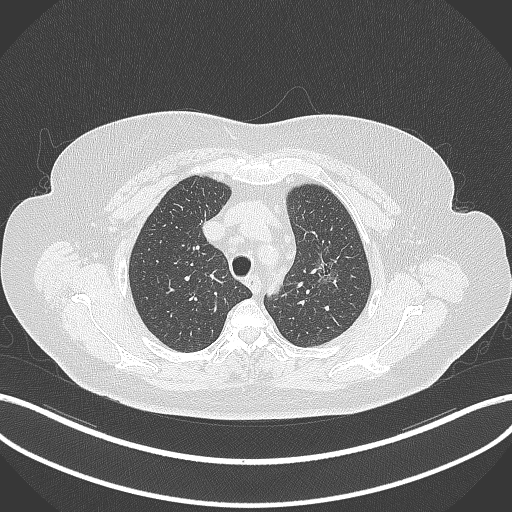
Chest CT, one axial slice. Slice 267 of 309 in the series (ordered by position). 120 kVp. Lung window (W 1500 / L -600 HU). 1 mm slice thickness. 512 × 512 image matrix. Female patient, age 70 years. From the clinical record (not read from this slice): clinical TNM (as recorded): T1c N0 M0.
Annotated regions visible in this slice (bounding box drawn by a radiologist):
- lung tumour (recorded histology: adenocarcinoma): box from (x=310, y=252) to (x=341, y=288) px